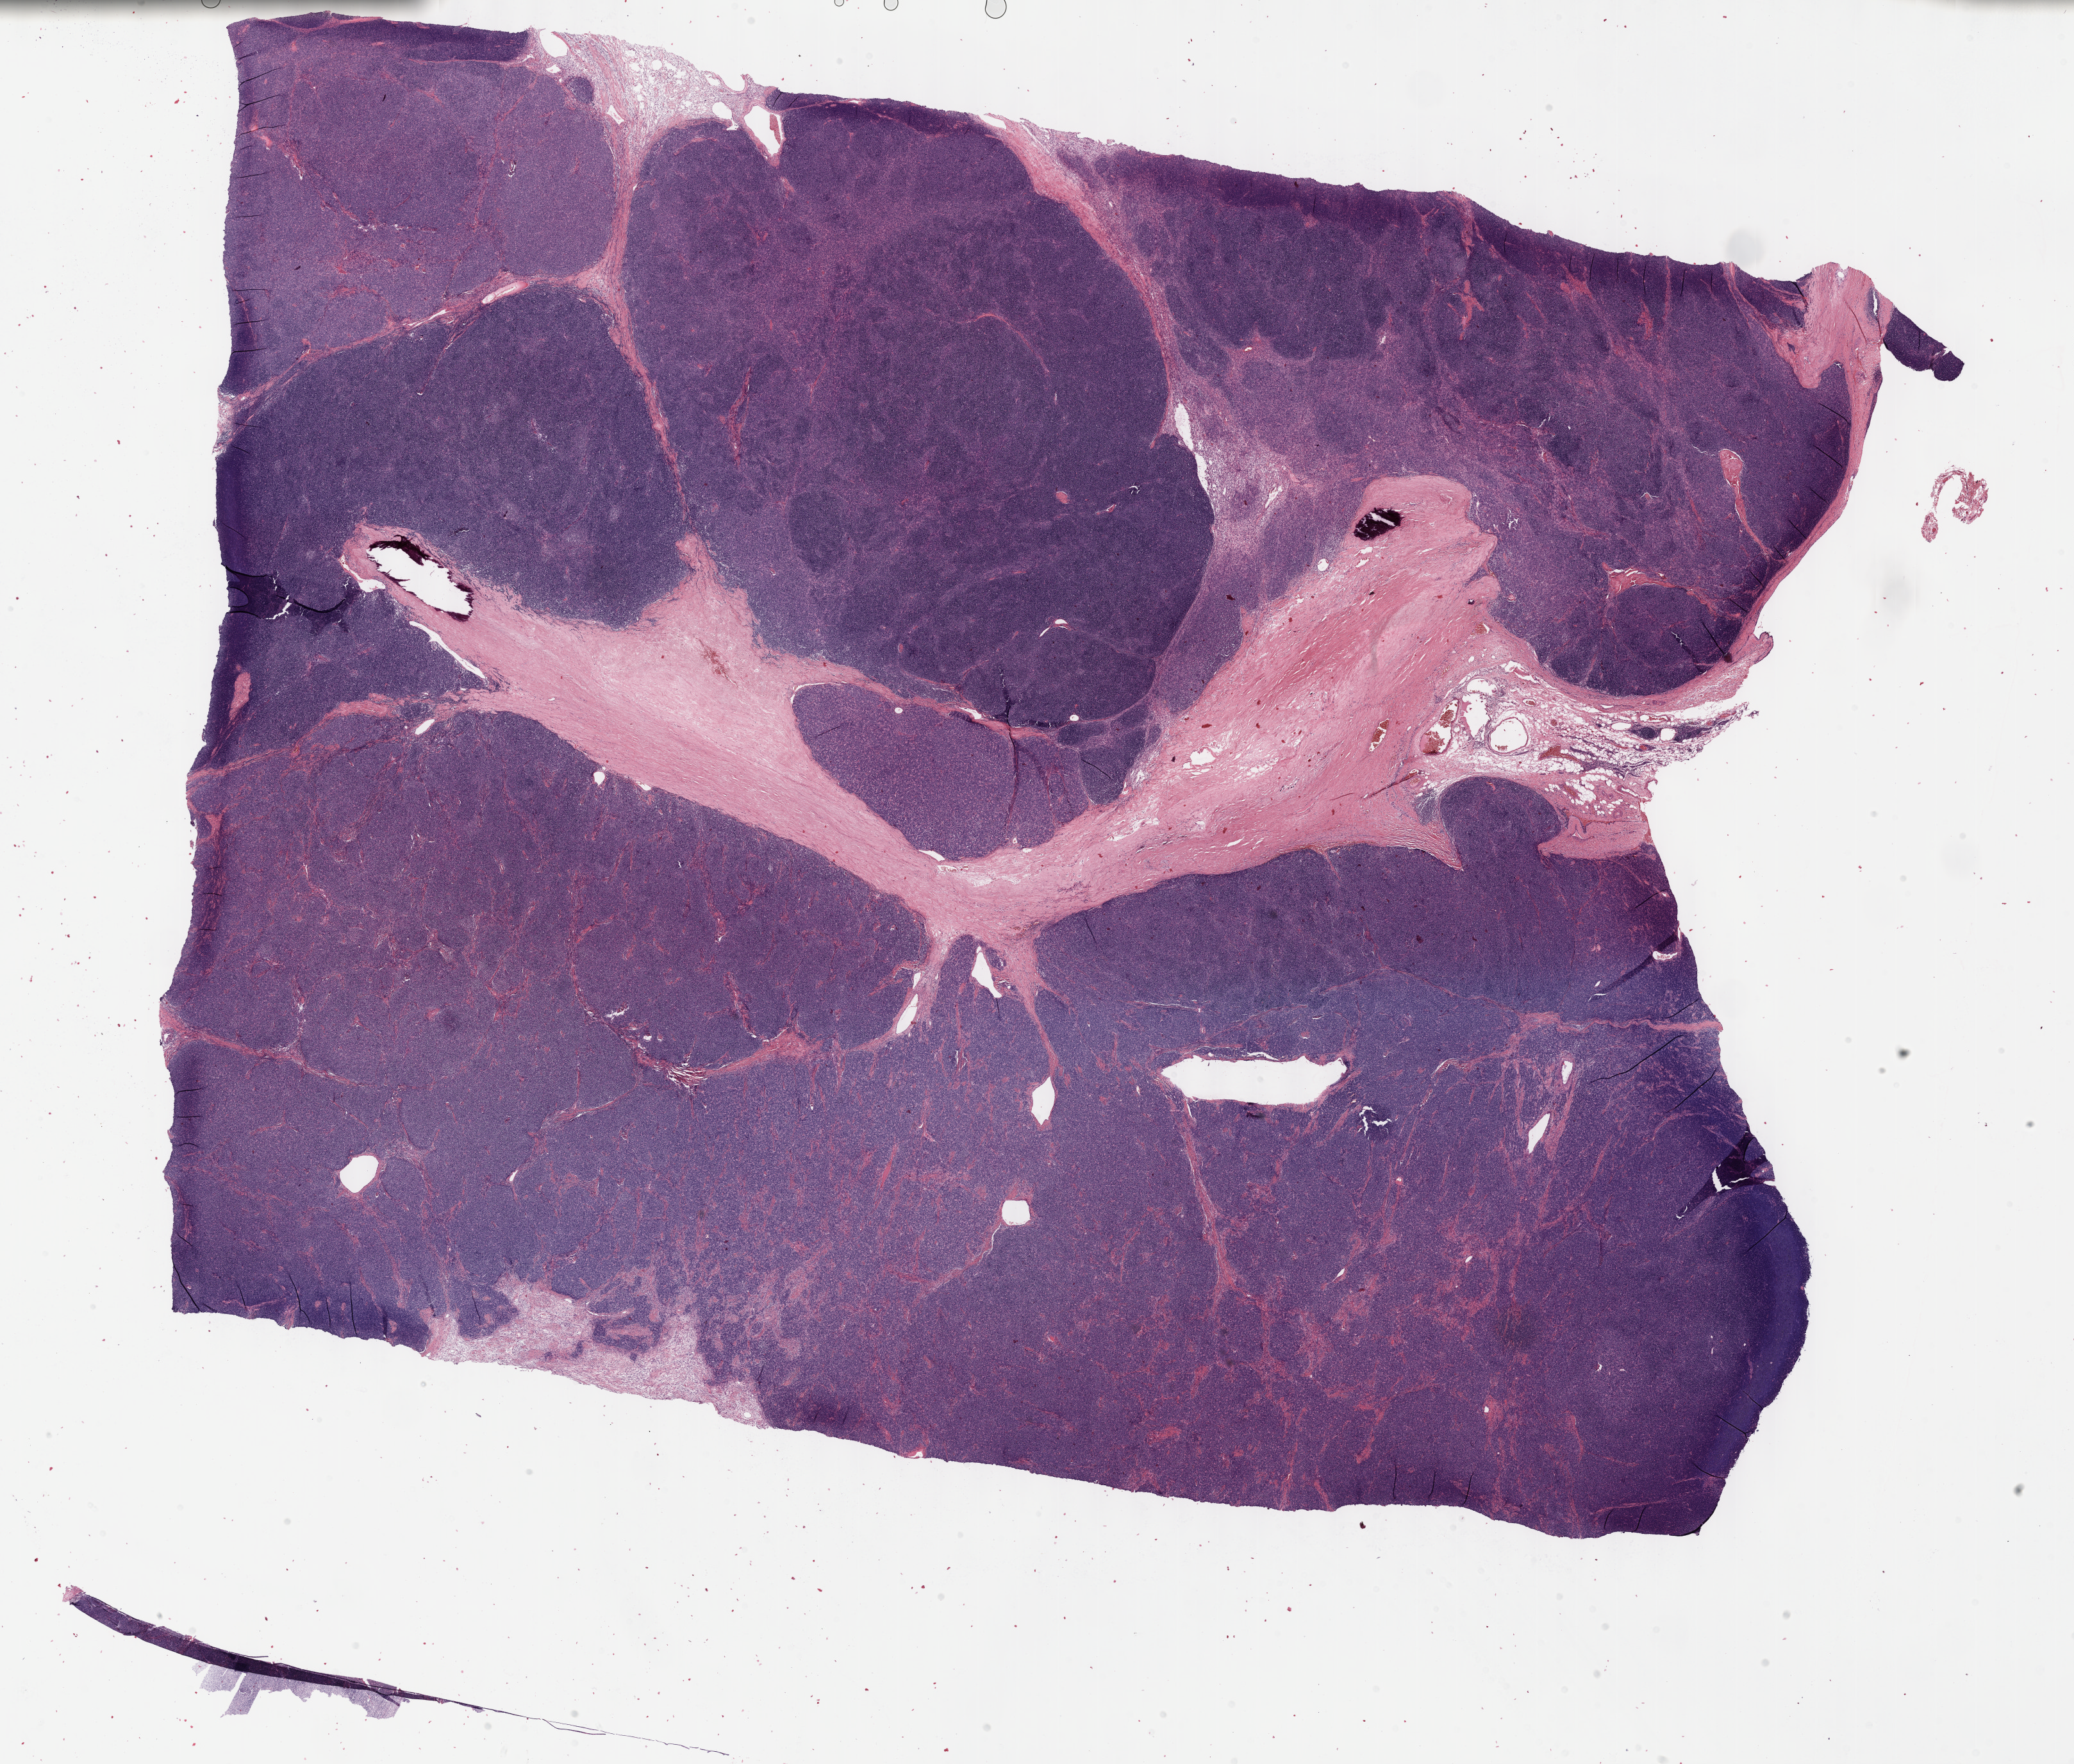
Digitized H&E tissue section (whole slide), low-resolution overview of the scanned area, about 26.2 x 22.3 mm (from a 40x scan). Formalin-fixed paraffin-embedded (FFPE) diagnostic section. Thymus, primary tumour sample. Male patient; age at initial diagnosis 69 years.
• pathologic diagnosis: Thymoma, type AB, NOS (anterior mediastinum)